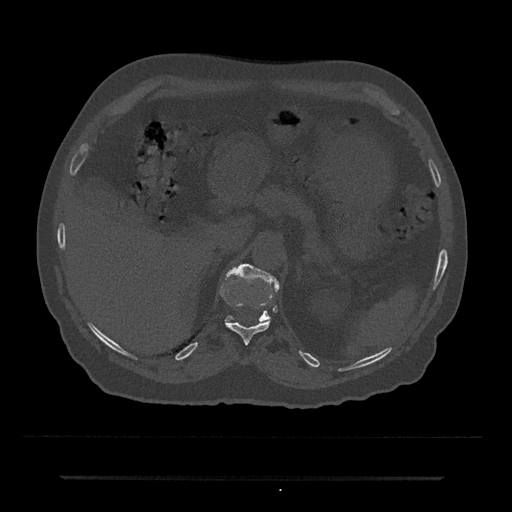
CT including the spine, one axial slice; slice 166 of 797 in the series (ordered by position); reconstruction kernel Br40s/3; 120 kVp; bone window (W 1800 / L 400 HU); 512 × 512 image matrix, field of view 437 × 437 mm. Patient: male, 69 years. From the clinical record (not read from this slice): primary cancer: prostate.
Outlined on this slice (semi-automatic segmentation, software-assisted and operator-edited):
- T11 vertebra: bounding box <226,302,270,345> (left, top, right, bottom; pixels)
- T12 vertebra: <225,264,280,322>